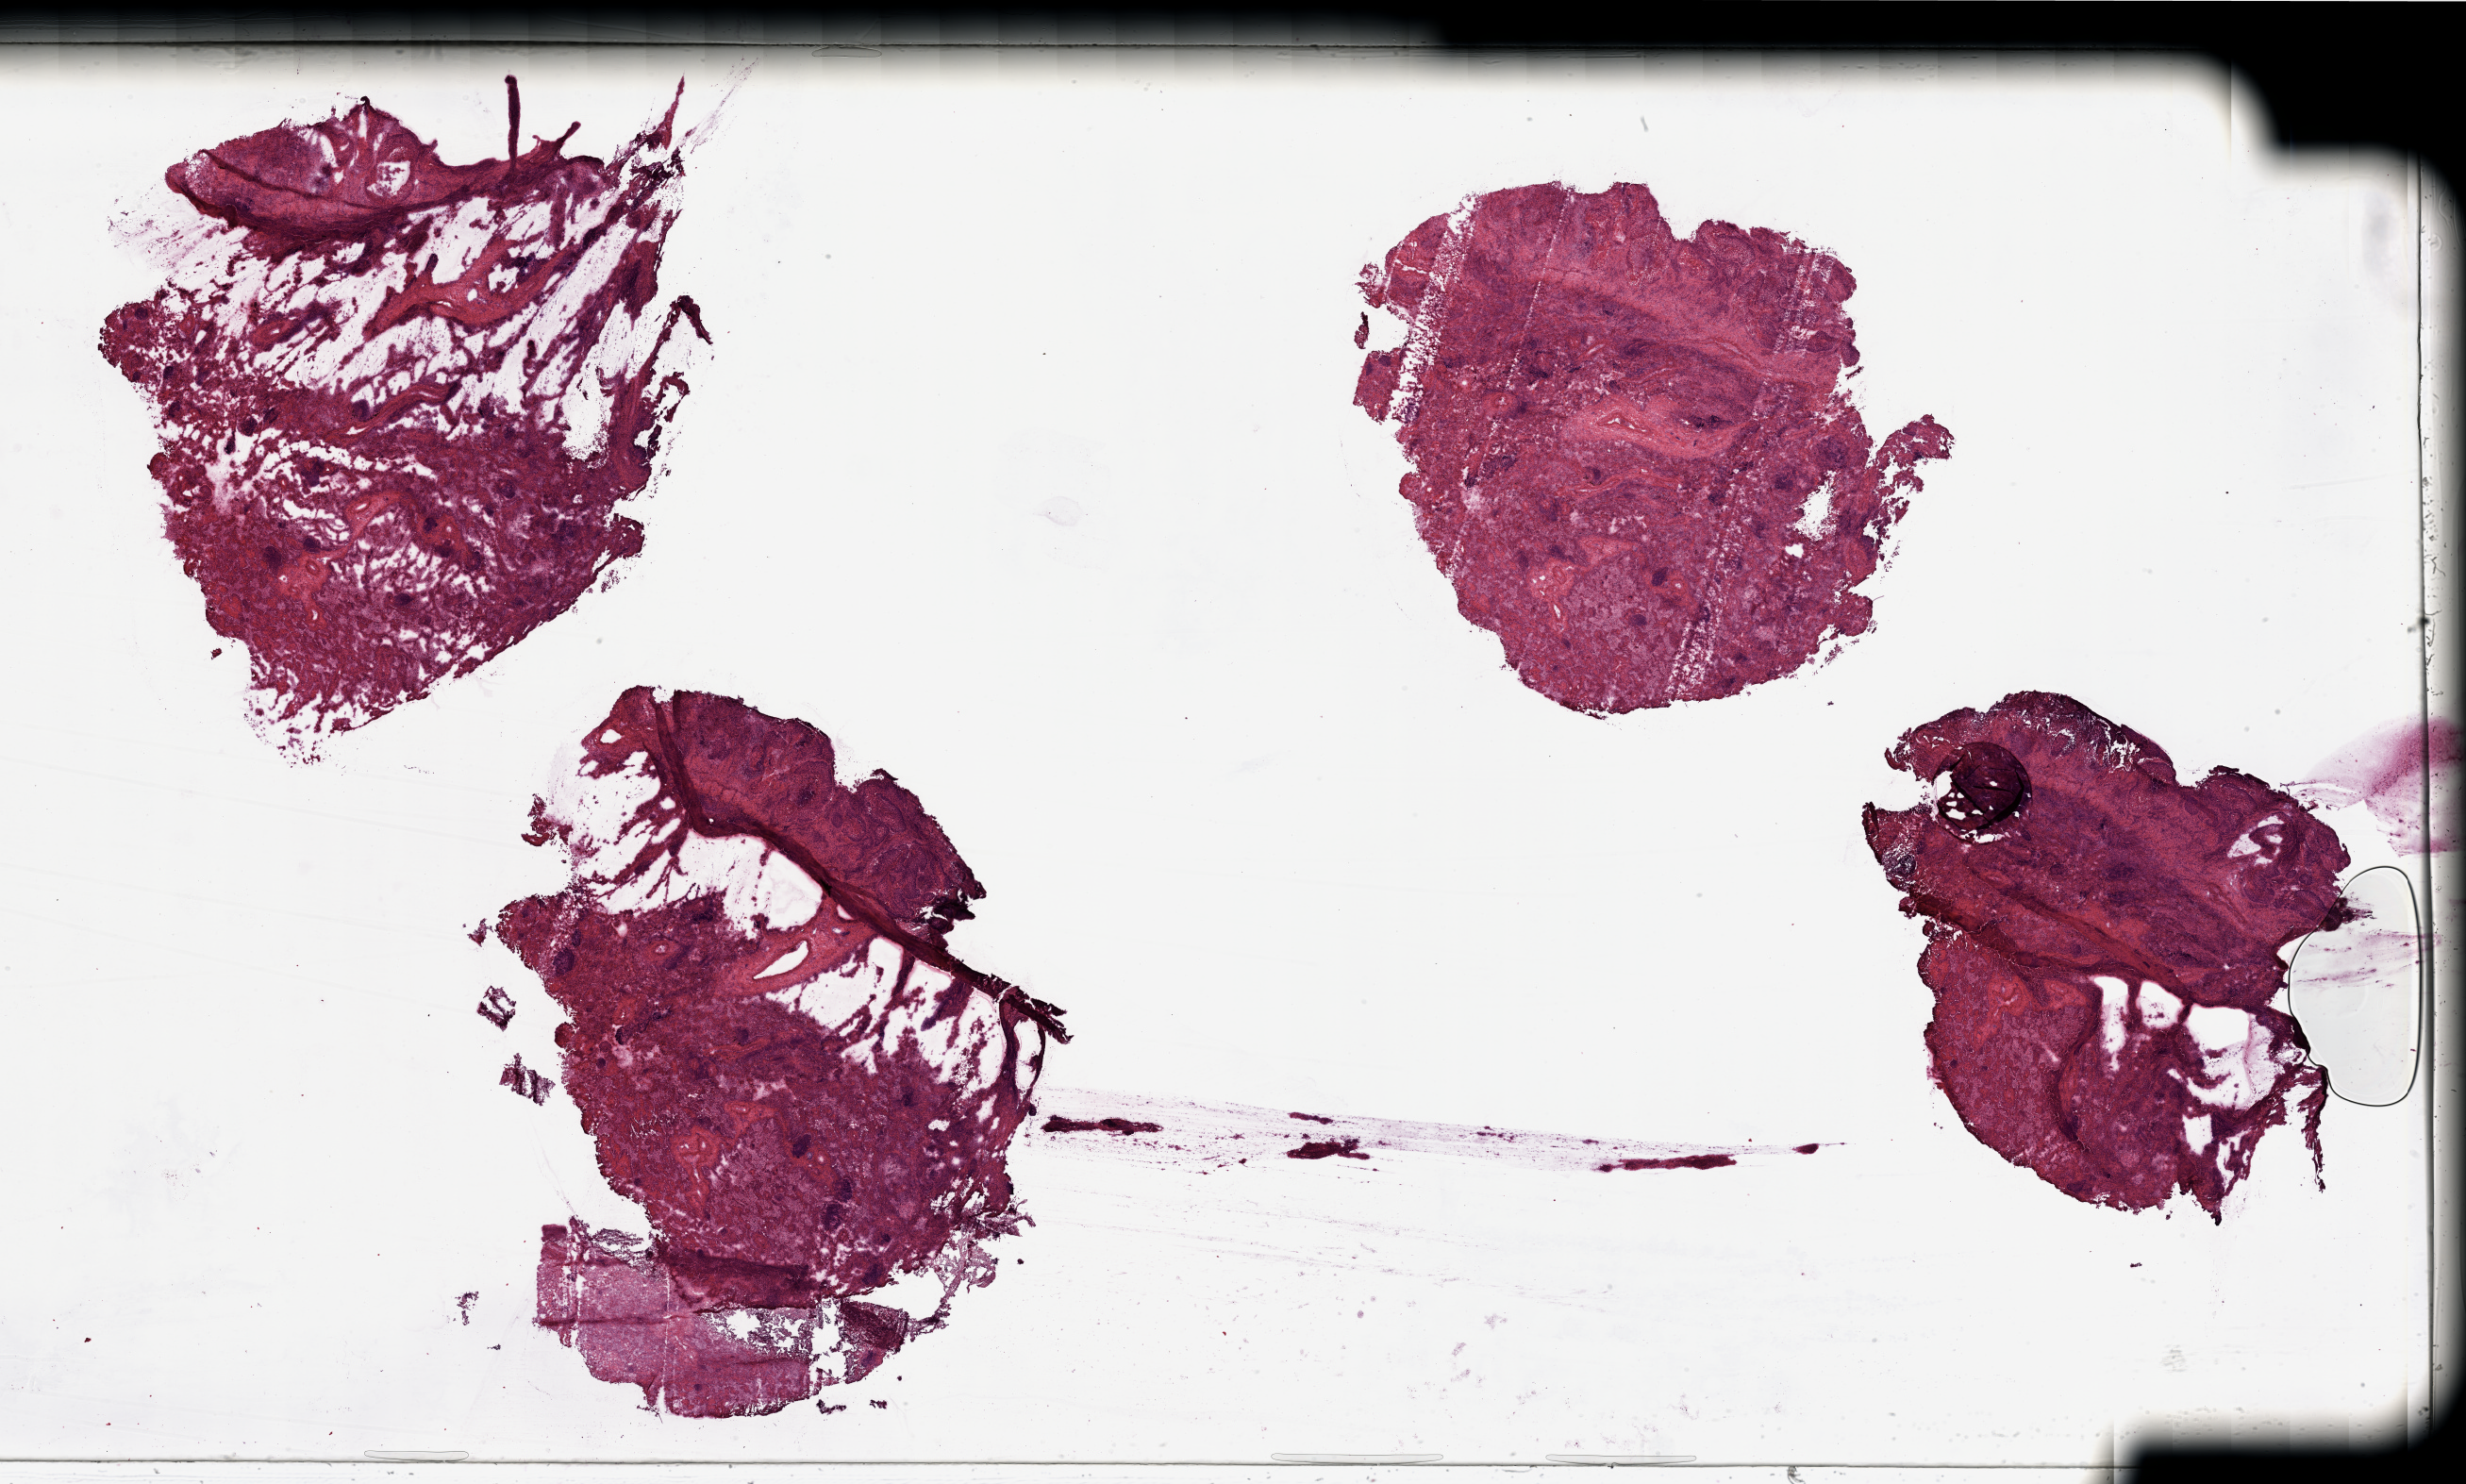
Digitized H&E-stained tissue section (whole slide) — shown as a low-resolution overview of the whole scanned area (about 41.3 x 24.9 mm, acquisition: 20x scan); tumour tissue sample, lung. Male, 65 y/o.
Primary tumour site (as recorded): left lower lobe. Patient diagnosis (cohort enrolment): squamous cell carcinoma (lung).